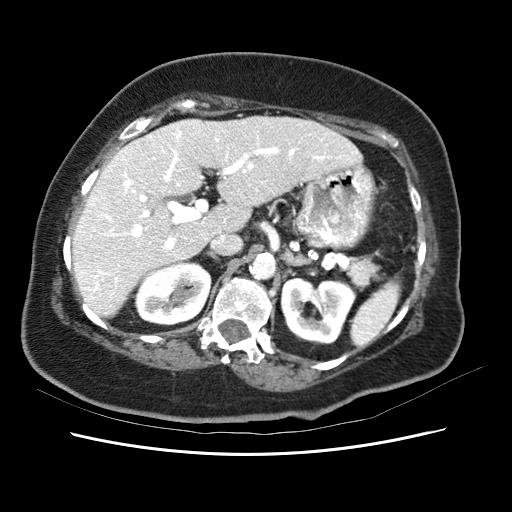
Contrast-enhanced abdominal CT (liver protocol), one axial slice. Position 36 of 62 along the scan axis. Reconstruction kernel STANDARD. 120 kVp. Soft-tissue window (W 400 / L 40 HU). 512 × 512 image matrix, field of view 340 × 340 mm. From the clinical record (not read from this slice): diagnosis: hepatocellular carcinoma (patient treated with transarterial chemoembolisation; whether this scan precedes or follows treatment is not stated here); TNM stage (as recorded): Stage-I; Child-Pugh class: B; tumour nodularity: uninodular.
Annotated regions visible in this slice (semi-automatic segmentation, software-assisted and operator-edited):
- liver parenchyma outside the tumour (the mass and vessels are separate outlines, so this box may not span the whole liver): box from (x=72, y=115) to (x=364, y=318) px
- liver vessels: (x=88, y=133)–(x=356, y=282)